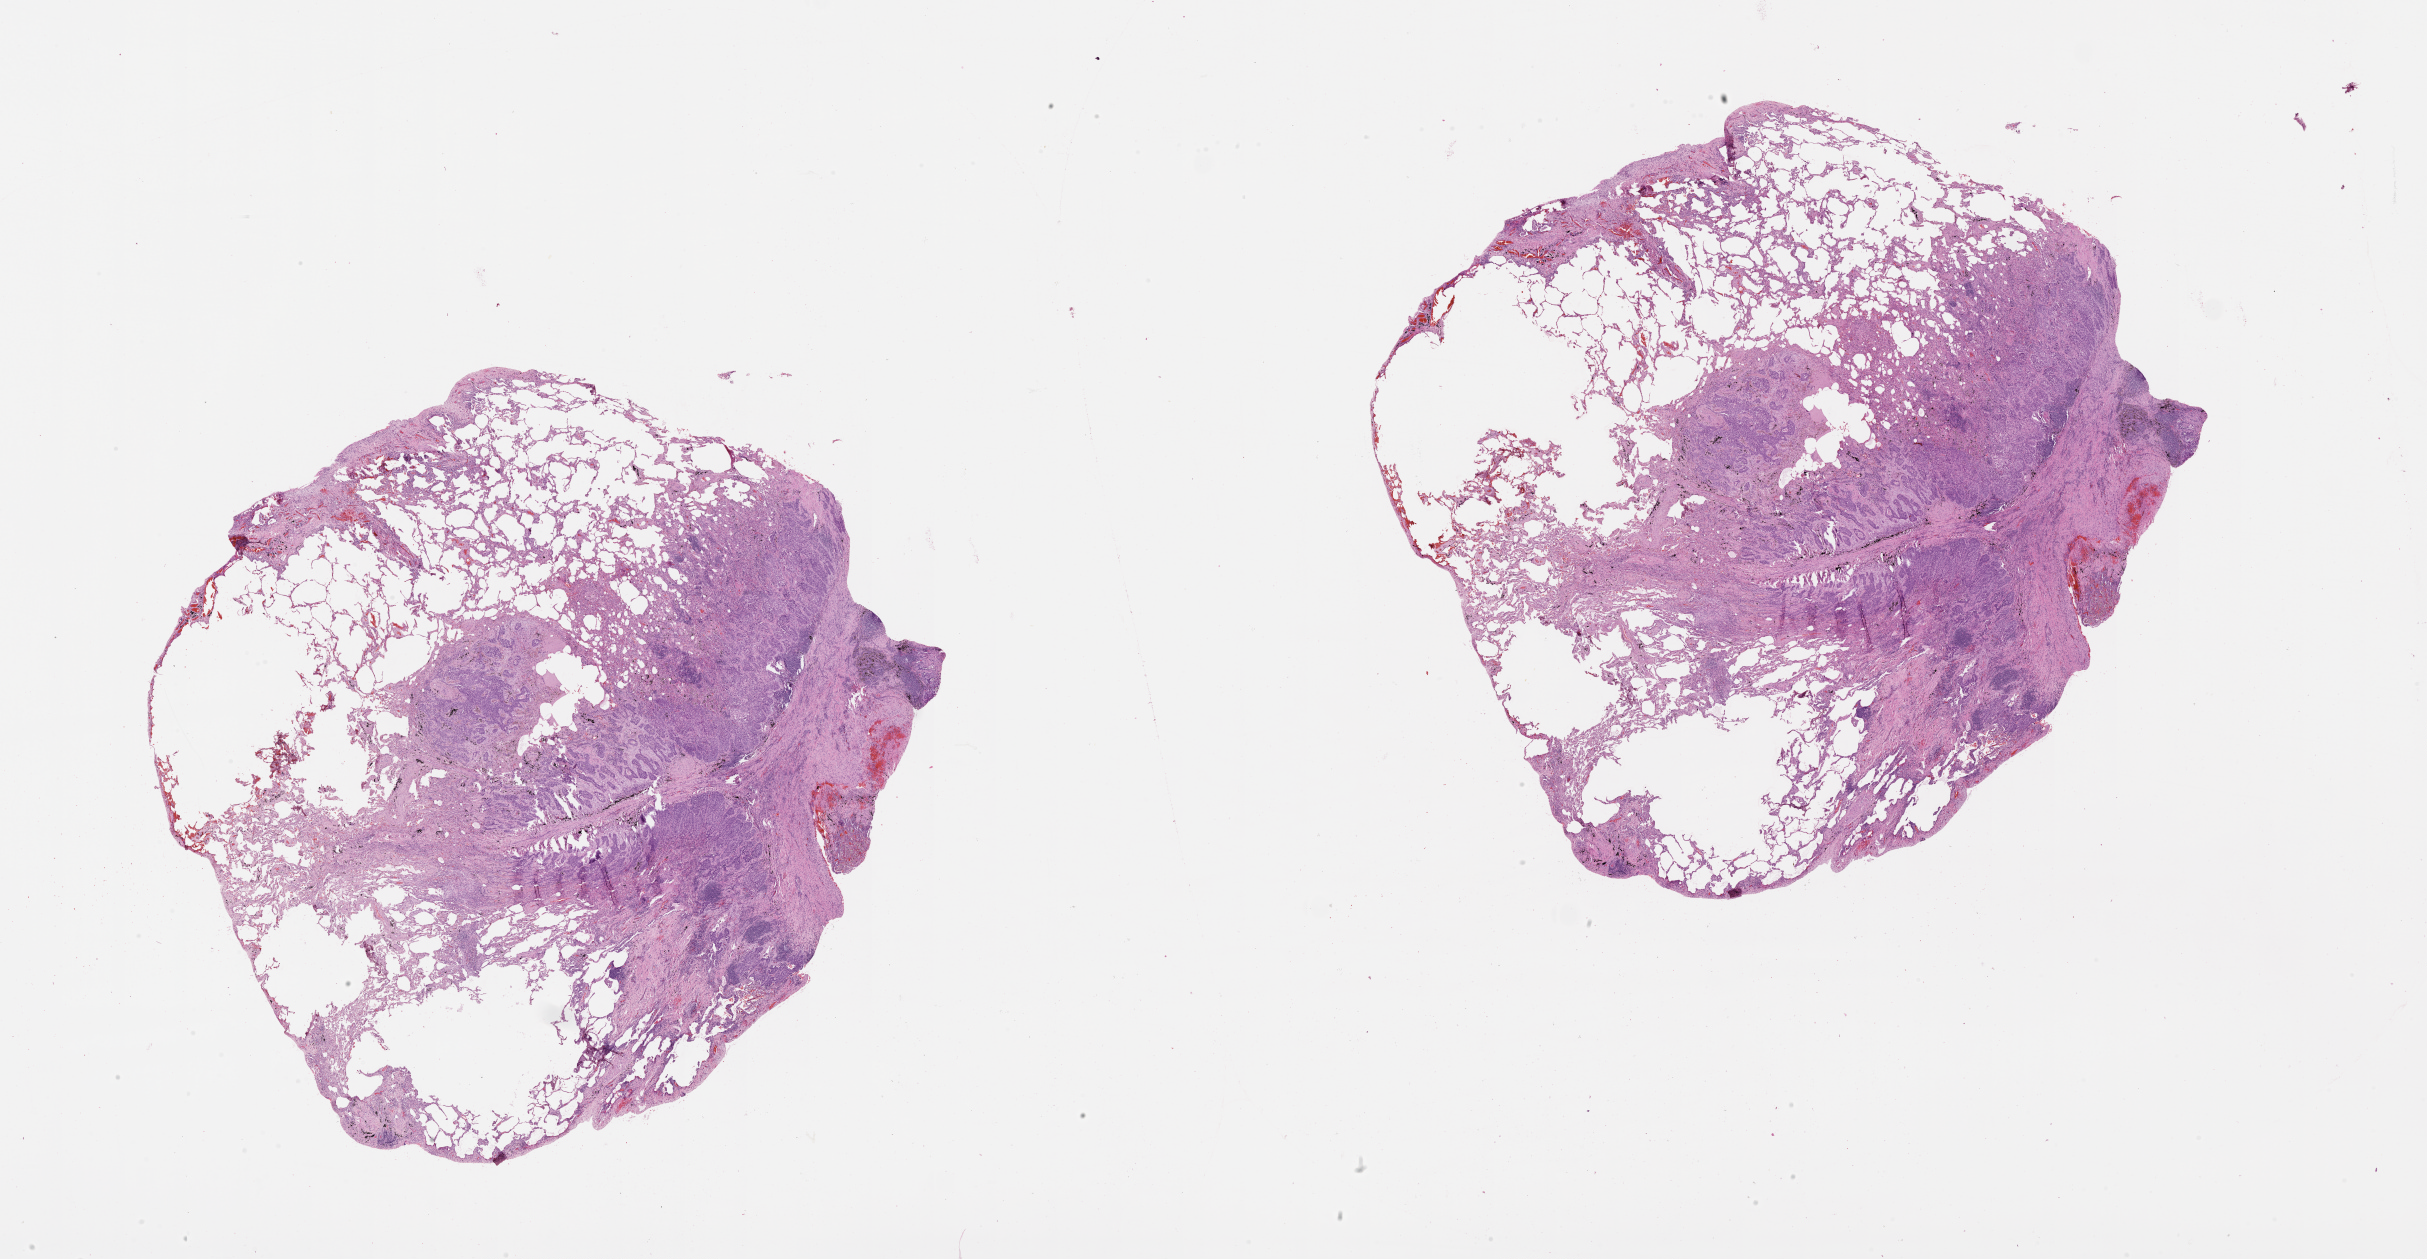
Hematoxylin and eosin (H&E) stained whole-slide image, shown as a low-resolution overview of the whole scanned area (about 39.1 x 20.3 mm, slide scanned at 20x); lung, tissue type not recorded.
Patient diagnosis (cohort enrolment): squamous cell carcinoma (lung).